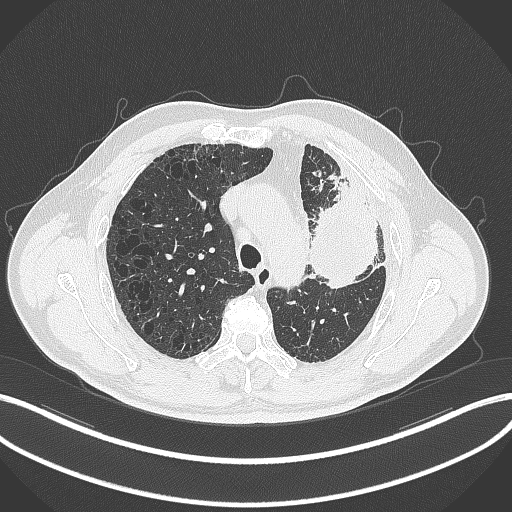
Chest CT, one axial slice; position 229 of 297 along the scan axis; reconstruction kernel B70f; lung window (W 1500 / L -600 HU); 1 mm slice thickness; 512 × 512 image matrix, field of view 400 × 400 mm. Patient: male, 68 years. From the clinical record (not read from this slice): clinical TNM (as recorded): T3 N3 M1.
Outlined on this slice (rectangle marked by the reading radiologist):
- lung tumour (recorded histology: adenocarcinoma): bounding box <301,177,378,299> (left, top, right, bottom; pixels)